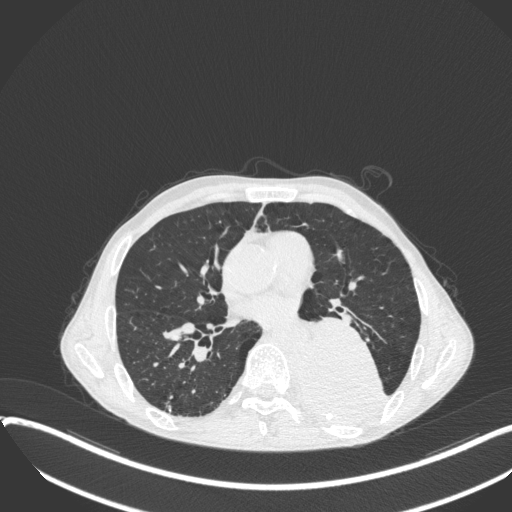
Chest CT, one axial slice. Slice 185 of 400 in the series (ordered by position). Reconstruction kernel B31f. 120 kVp. Lung window (W 1500 / L -600 HU). 512 × 512 image matrix, field of view 400 × 400 mm. Patient: male, 57 years. Case-level facts recorded for this patient, not image findings: clinical TNM (as recorded): T4 N0 M0.
Structures marked on this image (rectangle marked by the reading radiologist):
- lung tumour (recorded histology: squamous cell carcinoma): bounding box <290,314,391,426> (left, top, right, bottom; pixels)